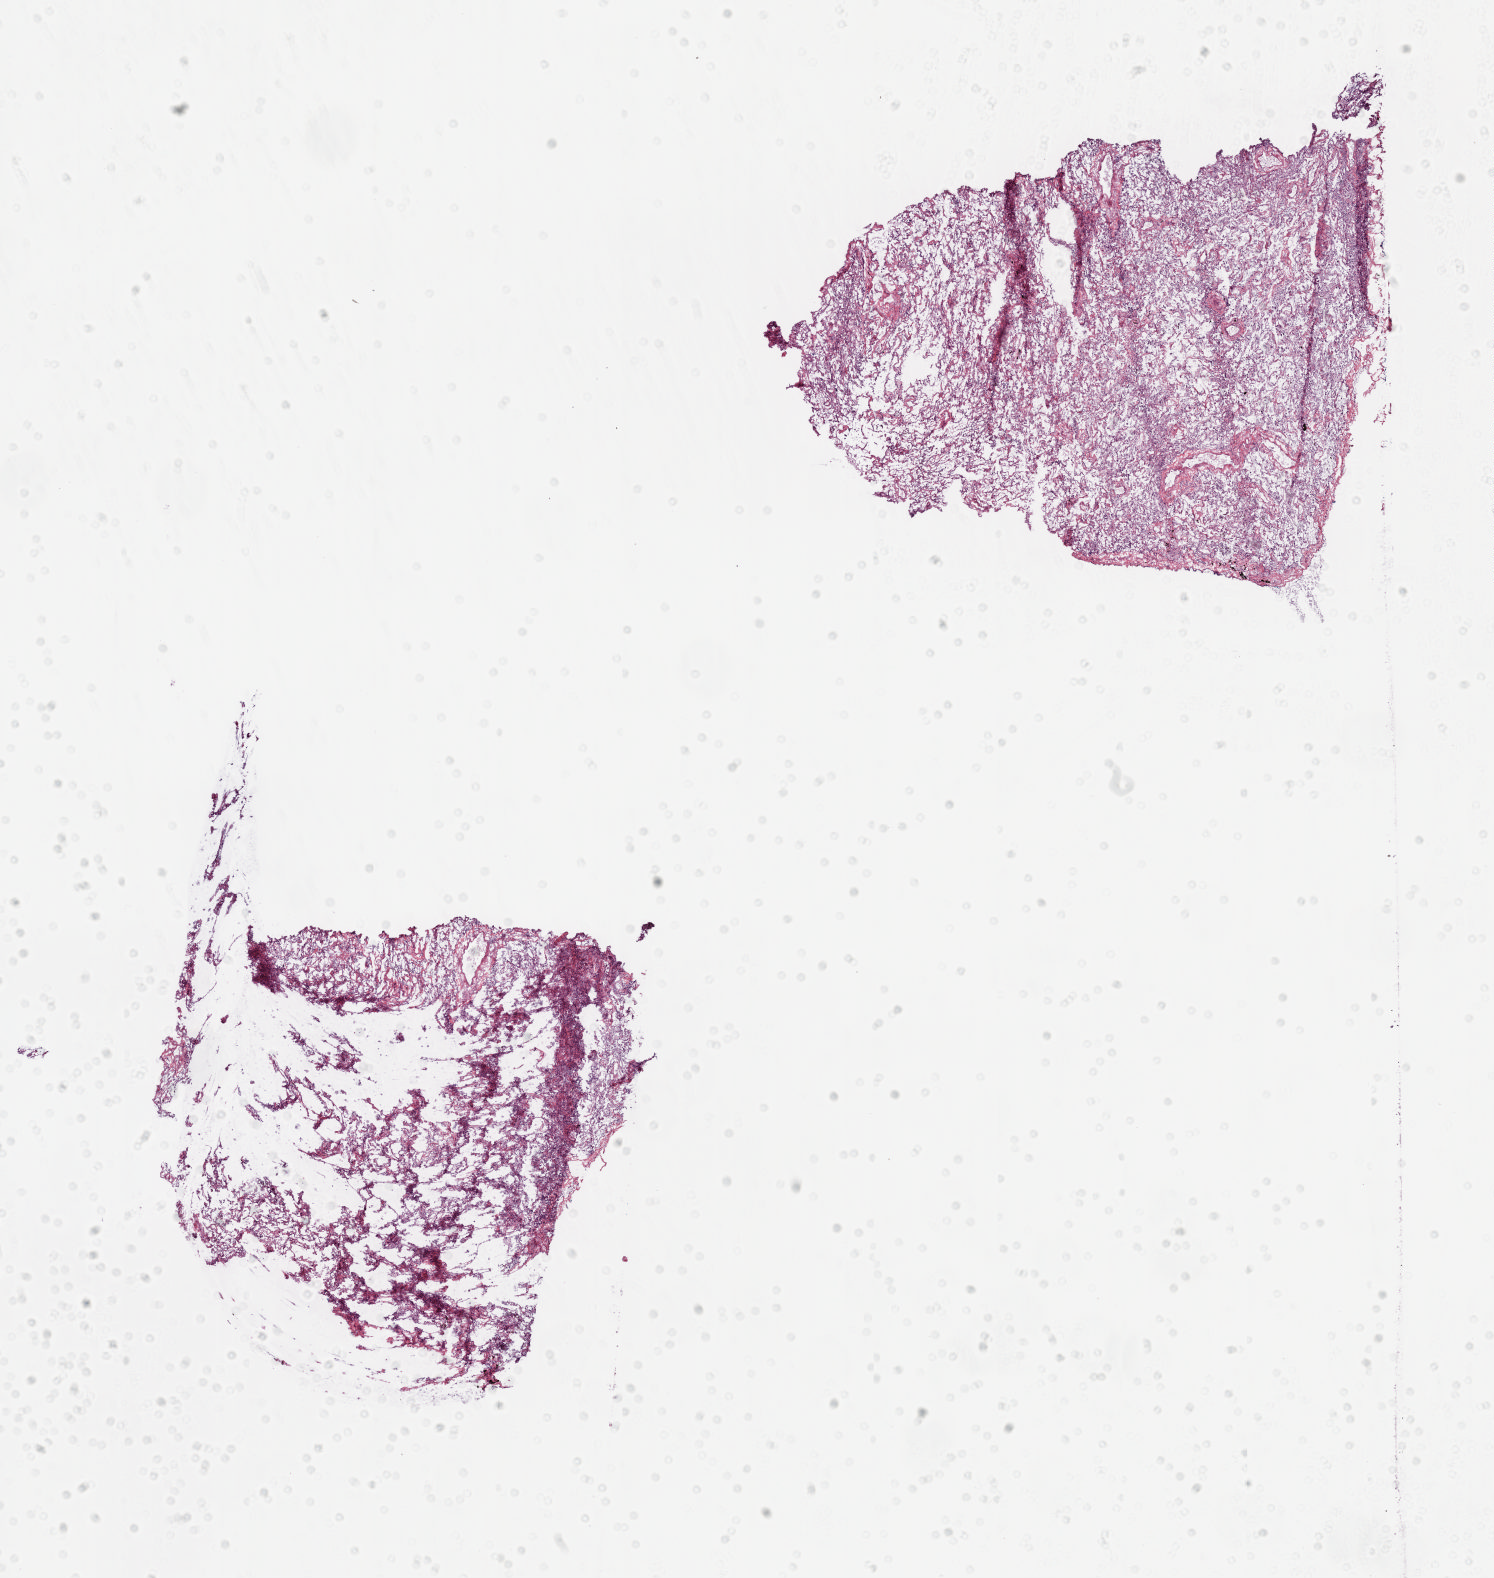
Hematoxylin and eosin (H&E) stained whole-slide image — whole scanned area (about 12.0 x 12.7 mm, acquisition: 20x scan) shown as a low-resolution overview. Frozen section. Solid tissue normal (non-tumour tissue) sample from the lung. Female, age 58 years at initial diagnosis.
- this section: solid tissue normal (non-tumour) sample from the same patient
- patient diagnosis: Adenocarcinoma, NOS (upper lobe, lung)